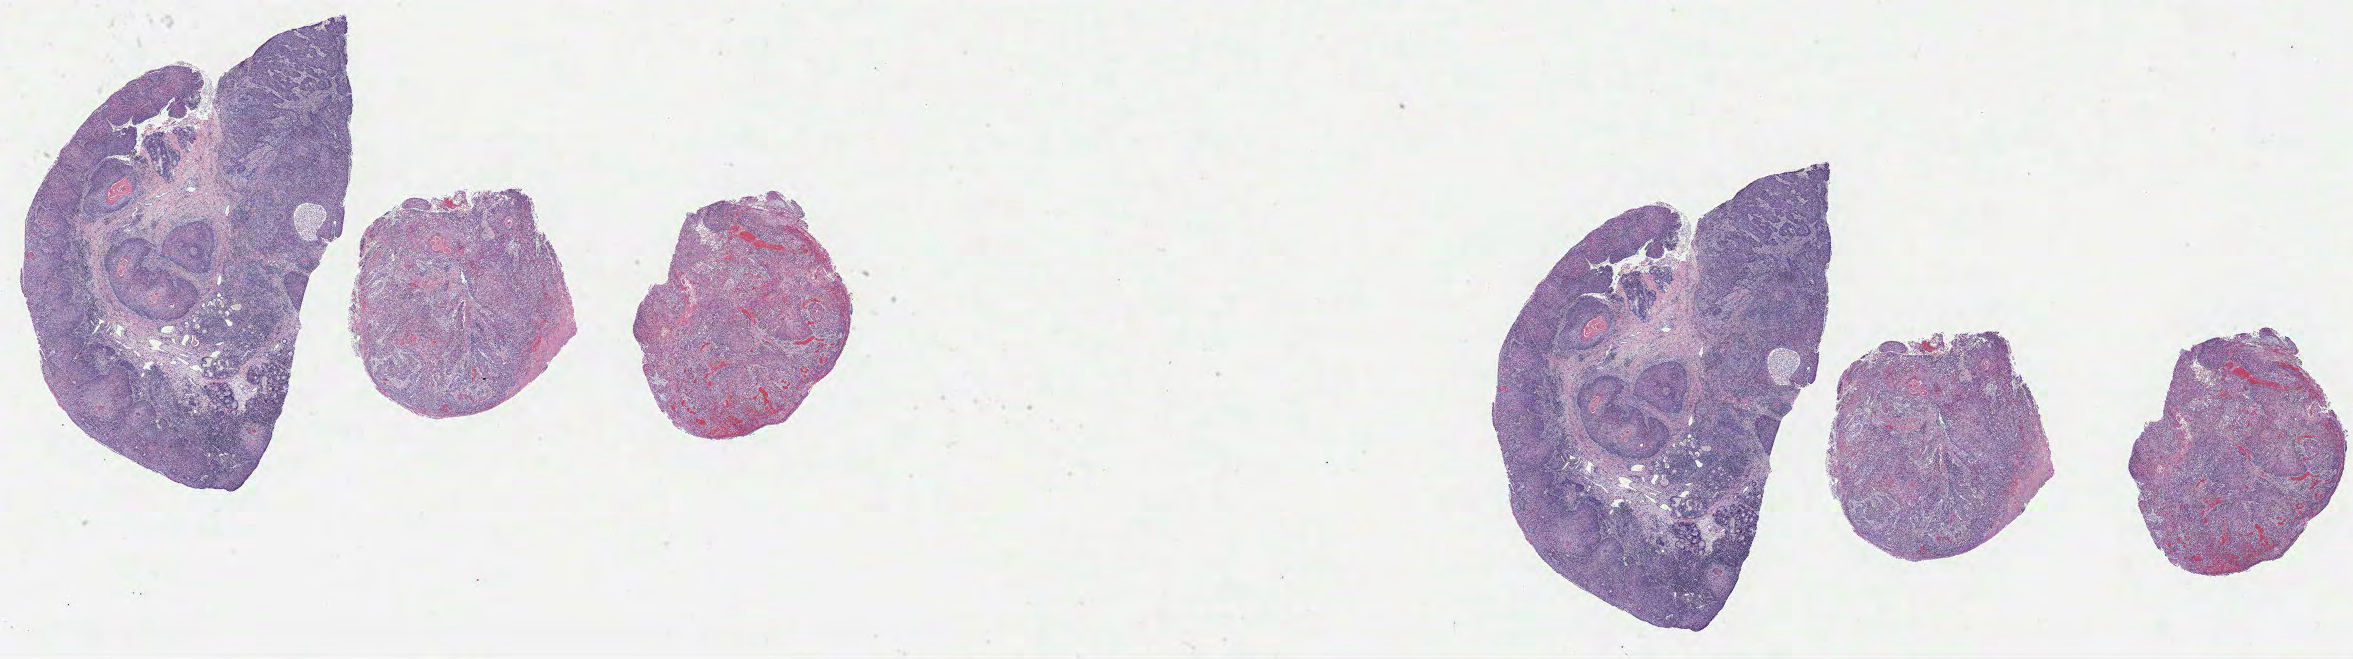
Whole-slide histology image, H&E-stained — shown as a low-resolution overview of the whole scanned area (about 38.0 x 10.6 mm); formalin-fixed paraffin-embedded (FFPE) diagnostic section; head and neck, primary tumour sample. Male, age 53 years at initial diagnosis.
Histologic diagnosis: Squamous cell carcinoma, NOS (larynx, NOS).